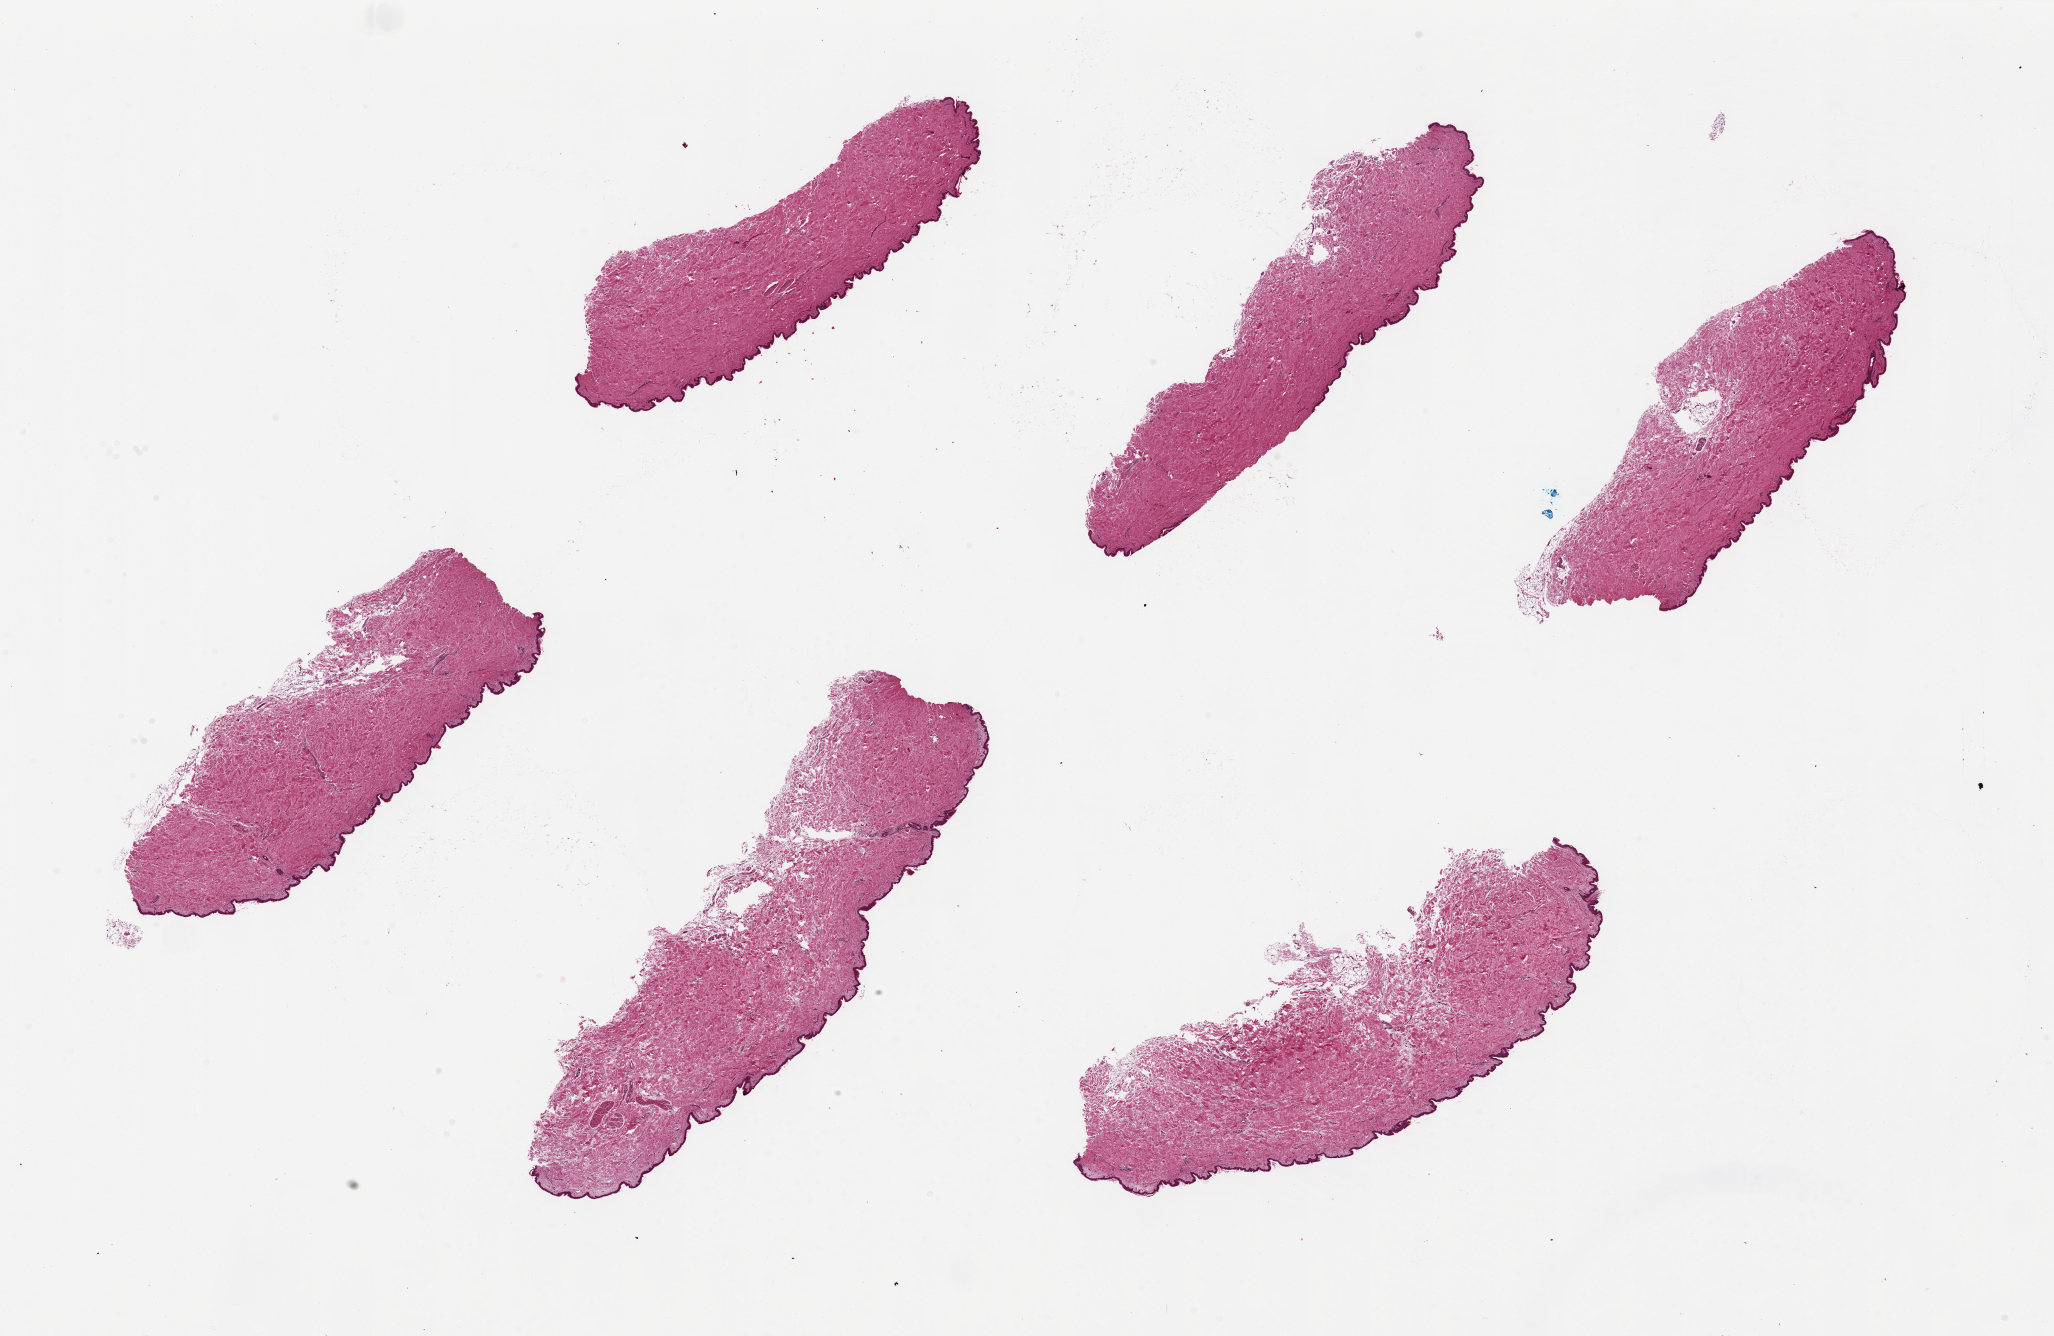
Digitized hematoxylin and eosin (H&E)-stained section, shown as a low-resolution overview of the whole scanned area (about 32.5 x 21.1 mm, slide scanned at 20x); PAXgene-fixed, paraffin-embedded tissue; sampled site (target tissue): skin of suprapubic region; donor tissue sample. Female donor.
Reviewer comment on this tissue sample: 6 pieces, up to 10x3mm; ~2% squamous epithelium.